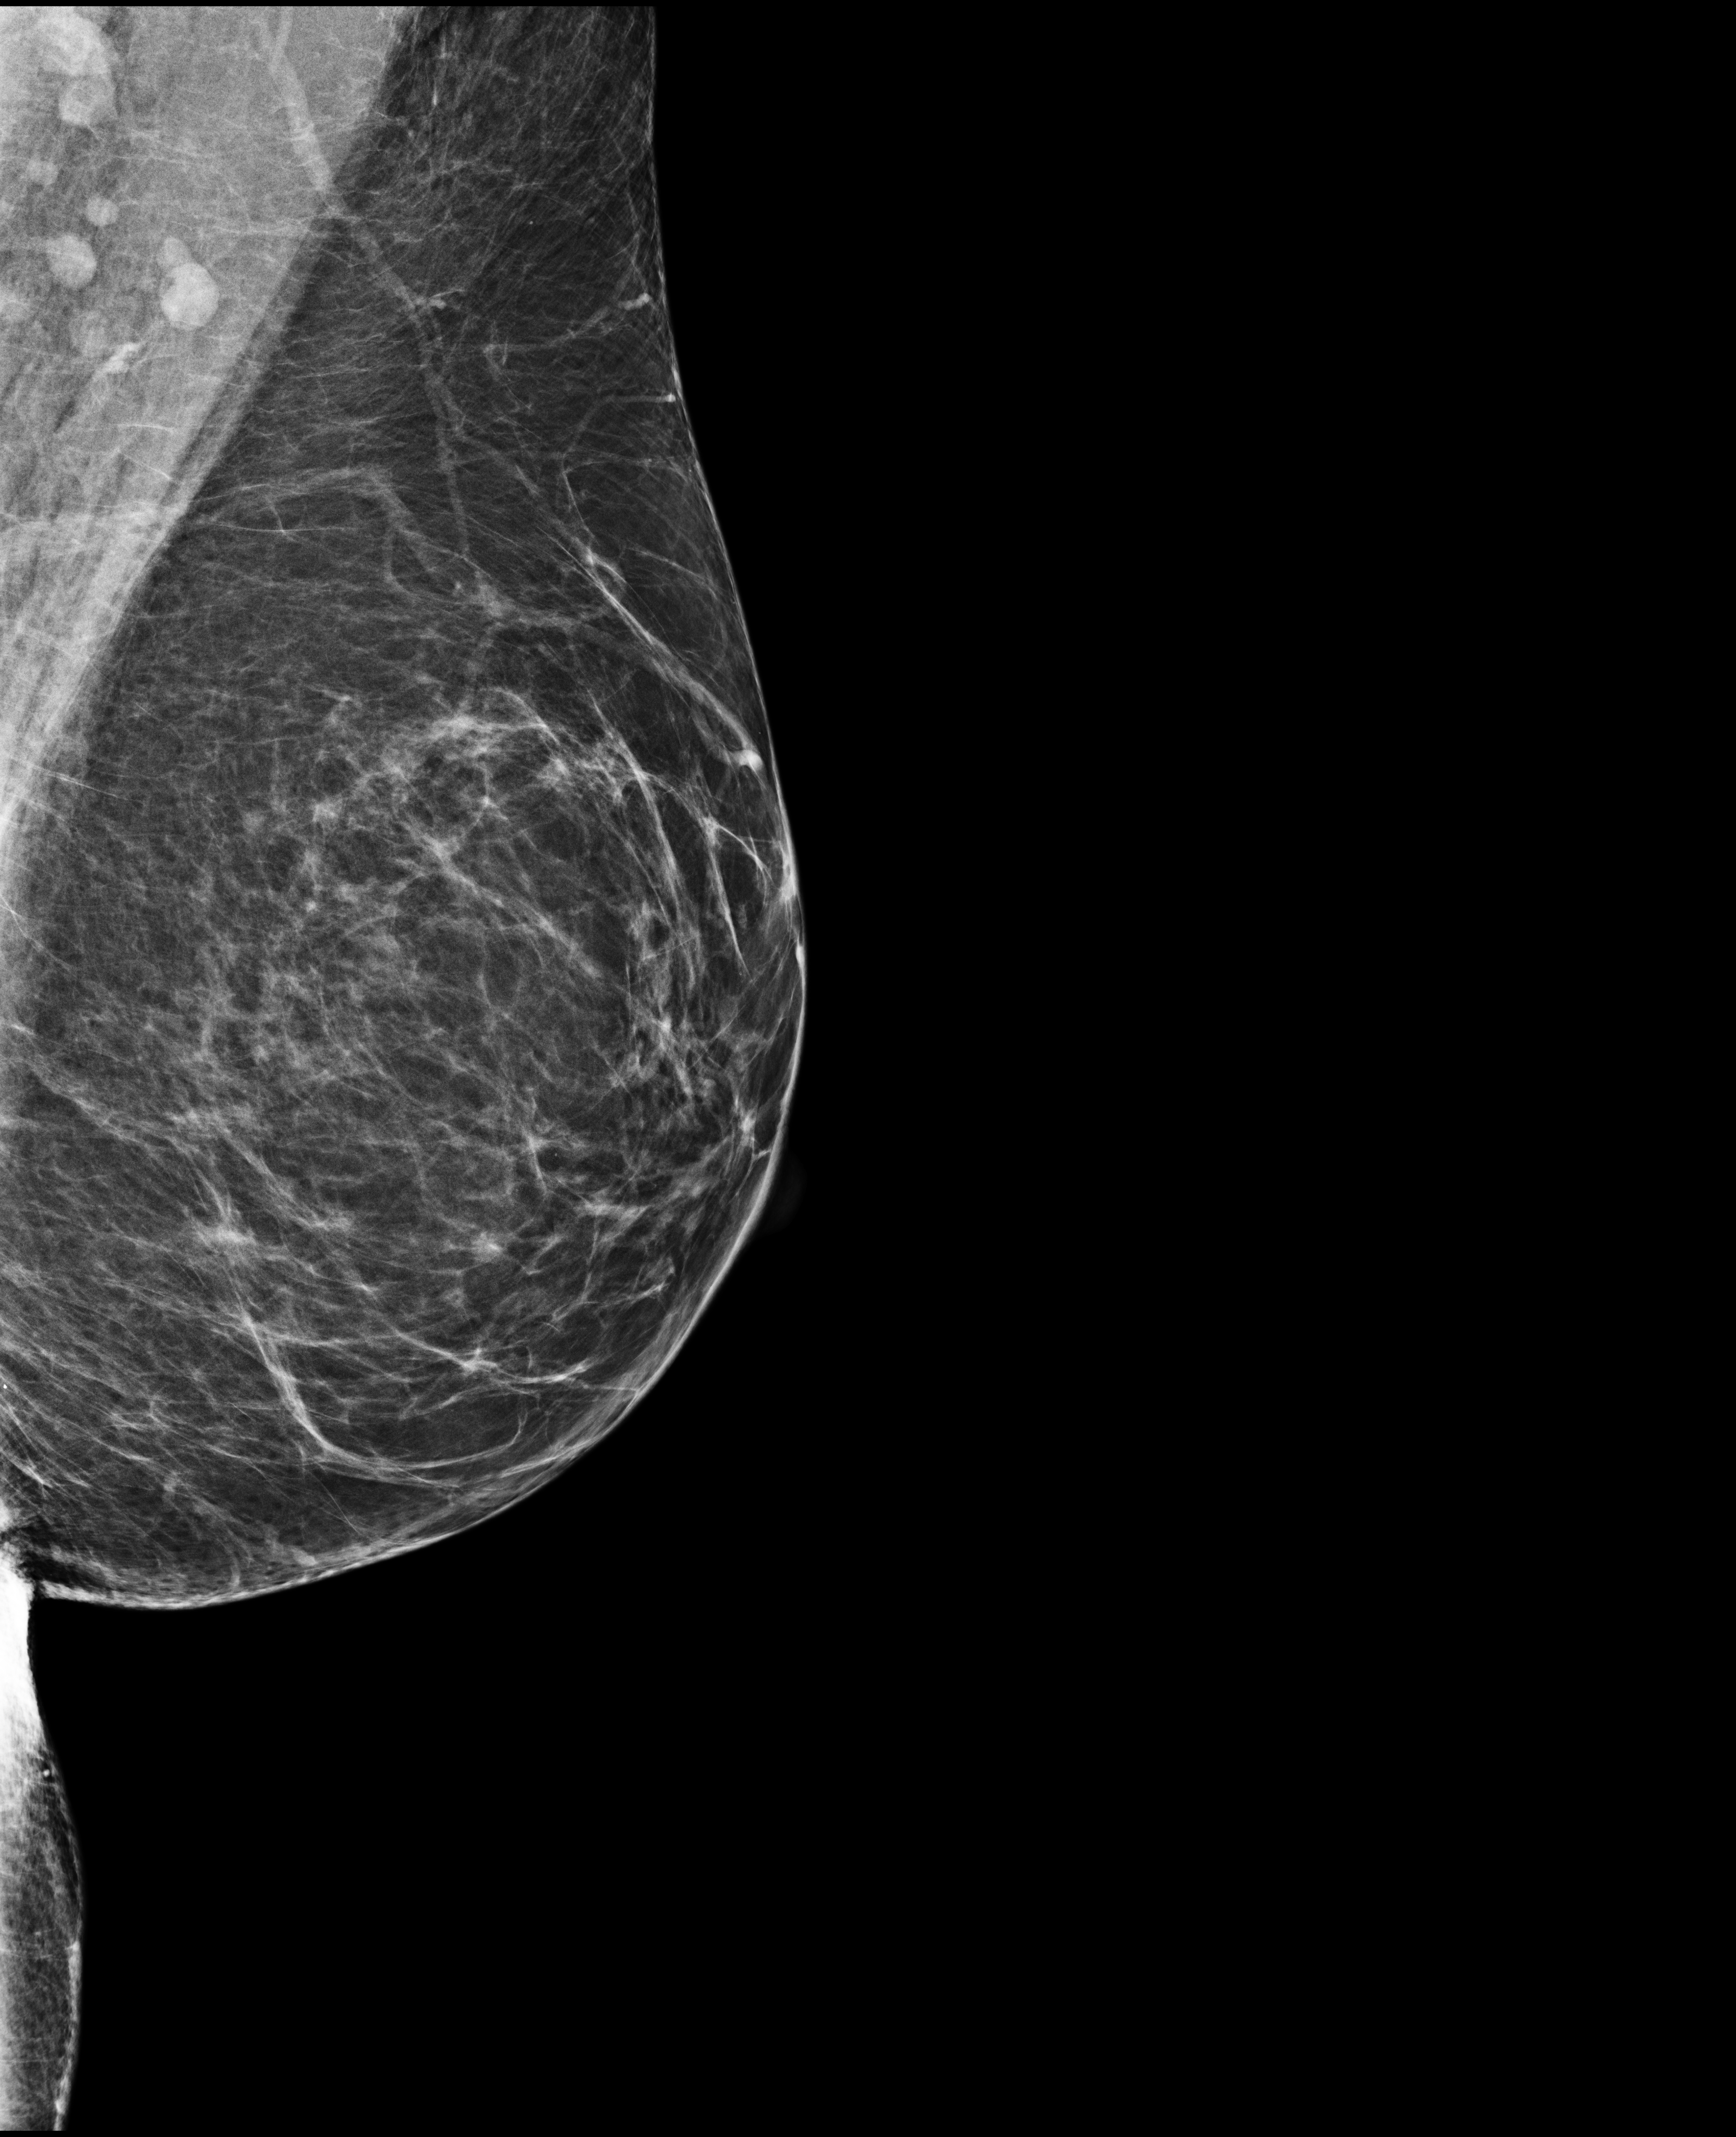
Full-field digital mammogram (FFDM), left breast, mediolateral oblique (MLO) view, annual screening mammography examination, compressed breast thickness 66 mm. Patient: female, 54 years.
BI-RADS breast density category at the screening exam (both breasts, scale 1–4): 3. Final BI-RADS category for the screening round (tomosynthesis exam, both breasts): category 2. Recall: recalled for additional imaging after this screen.